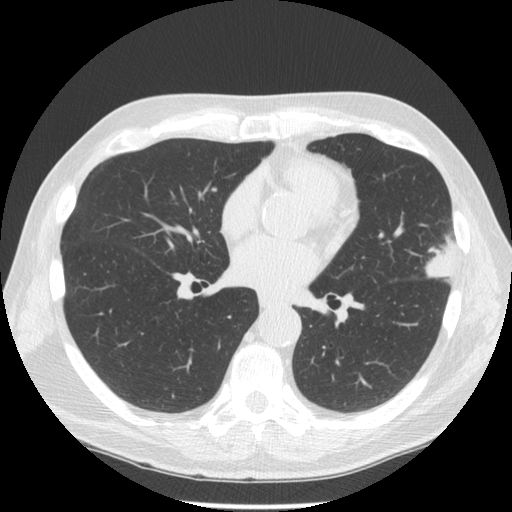
Low-dose screening chest CT, one axial slice. Slice 68 of 134 in the series (ordered by position). 120 kVp. Lung window (W 1500 / L -600 HU). 2.5 mm slice thickness. 512 × 512 image matrix, field of view 350 × 350 mm.
Outlined on this slice (outlined manually by an expert reader):
- lesion 1 (tumor, upper lobe of left lung): bounding box (x1, y1, x2, y2) in pixels: (426, 241, 458, 282)